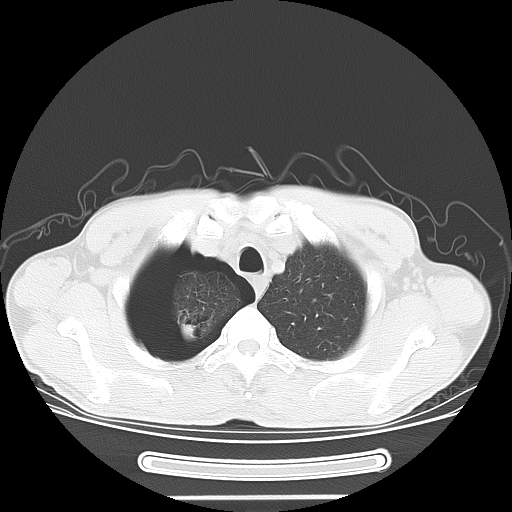
Chest CT, one axial slice. Position 58 of 67 along the scan axis. Reconstruction kernel LUNG. 120 kVp. Lung window (W 1500 / L -600 HU). 5 mm slice thickness. 512 × 512 image matrix, field of view 375 × 375 mm. Male patient. From the clinical record (not read from this slice): clinical TNM (as recorded): T1c N0 M0.
Structures marked on this image (bounding box drawn by a radiologist):
- lung tumour (recorded histology: adenocarcinoma): bounding box [x1, y1, x2, y2] px = [176, 319, 201, 346]